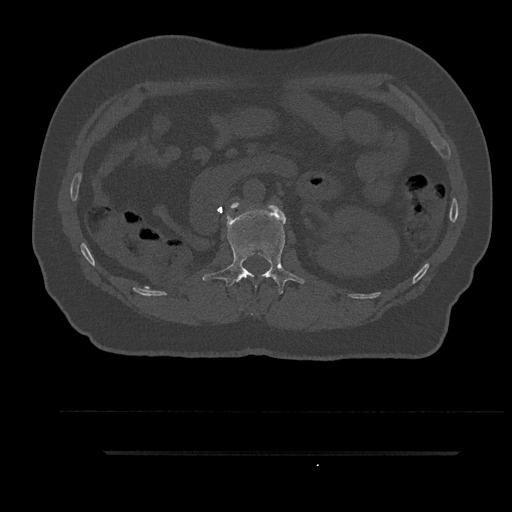
CT including the spine, one axial slice. Slice 175 of 797 in the series (ordered by position). 120 kVp. Bone window (W 1800 / L 400 HU). 512 × 512 image matrix, field of view 432 × 432 mm. Patient: male, 63 years. Case-level facts recorded for this patient, not image findings: primary cancer: renal.
Annotated regions visible in this slice (semi-automatic segmentation, software-assisted and operator-edited):
- L1 vertebra: bounding box <203,205,305,295> (left, top, right, bottom; pixels)
- L2 vertebra: <231,203,239,209>